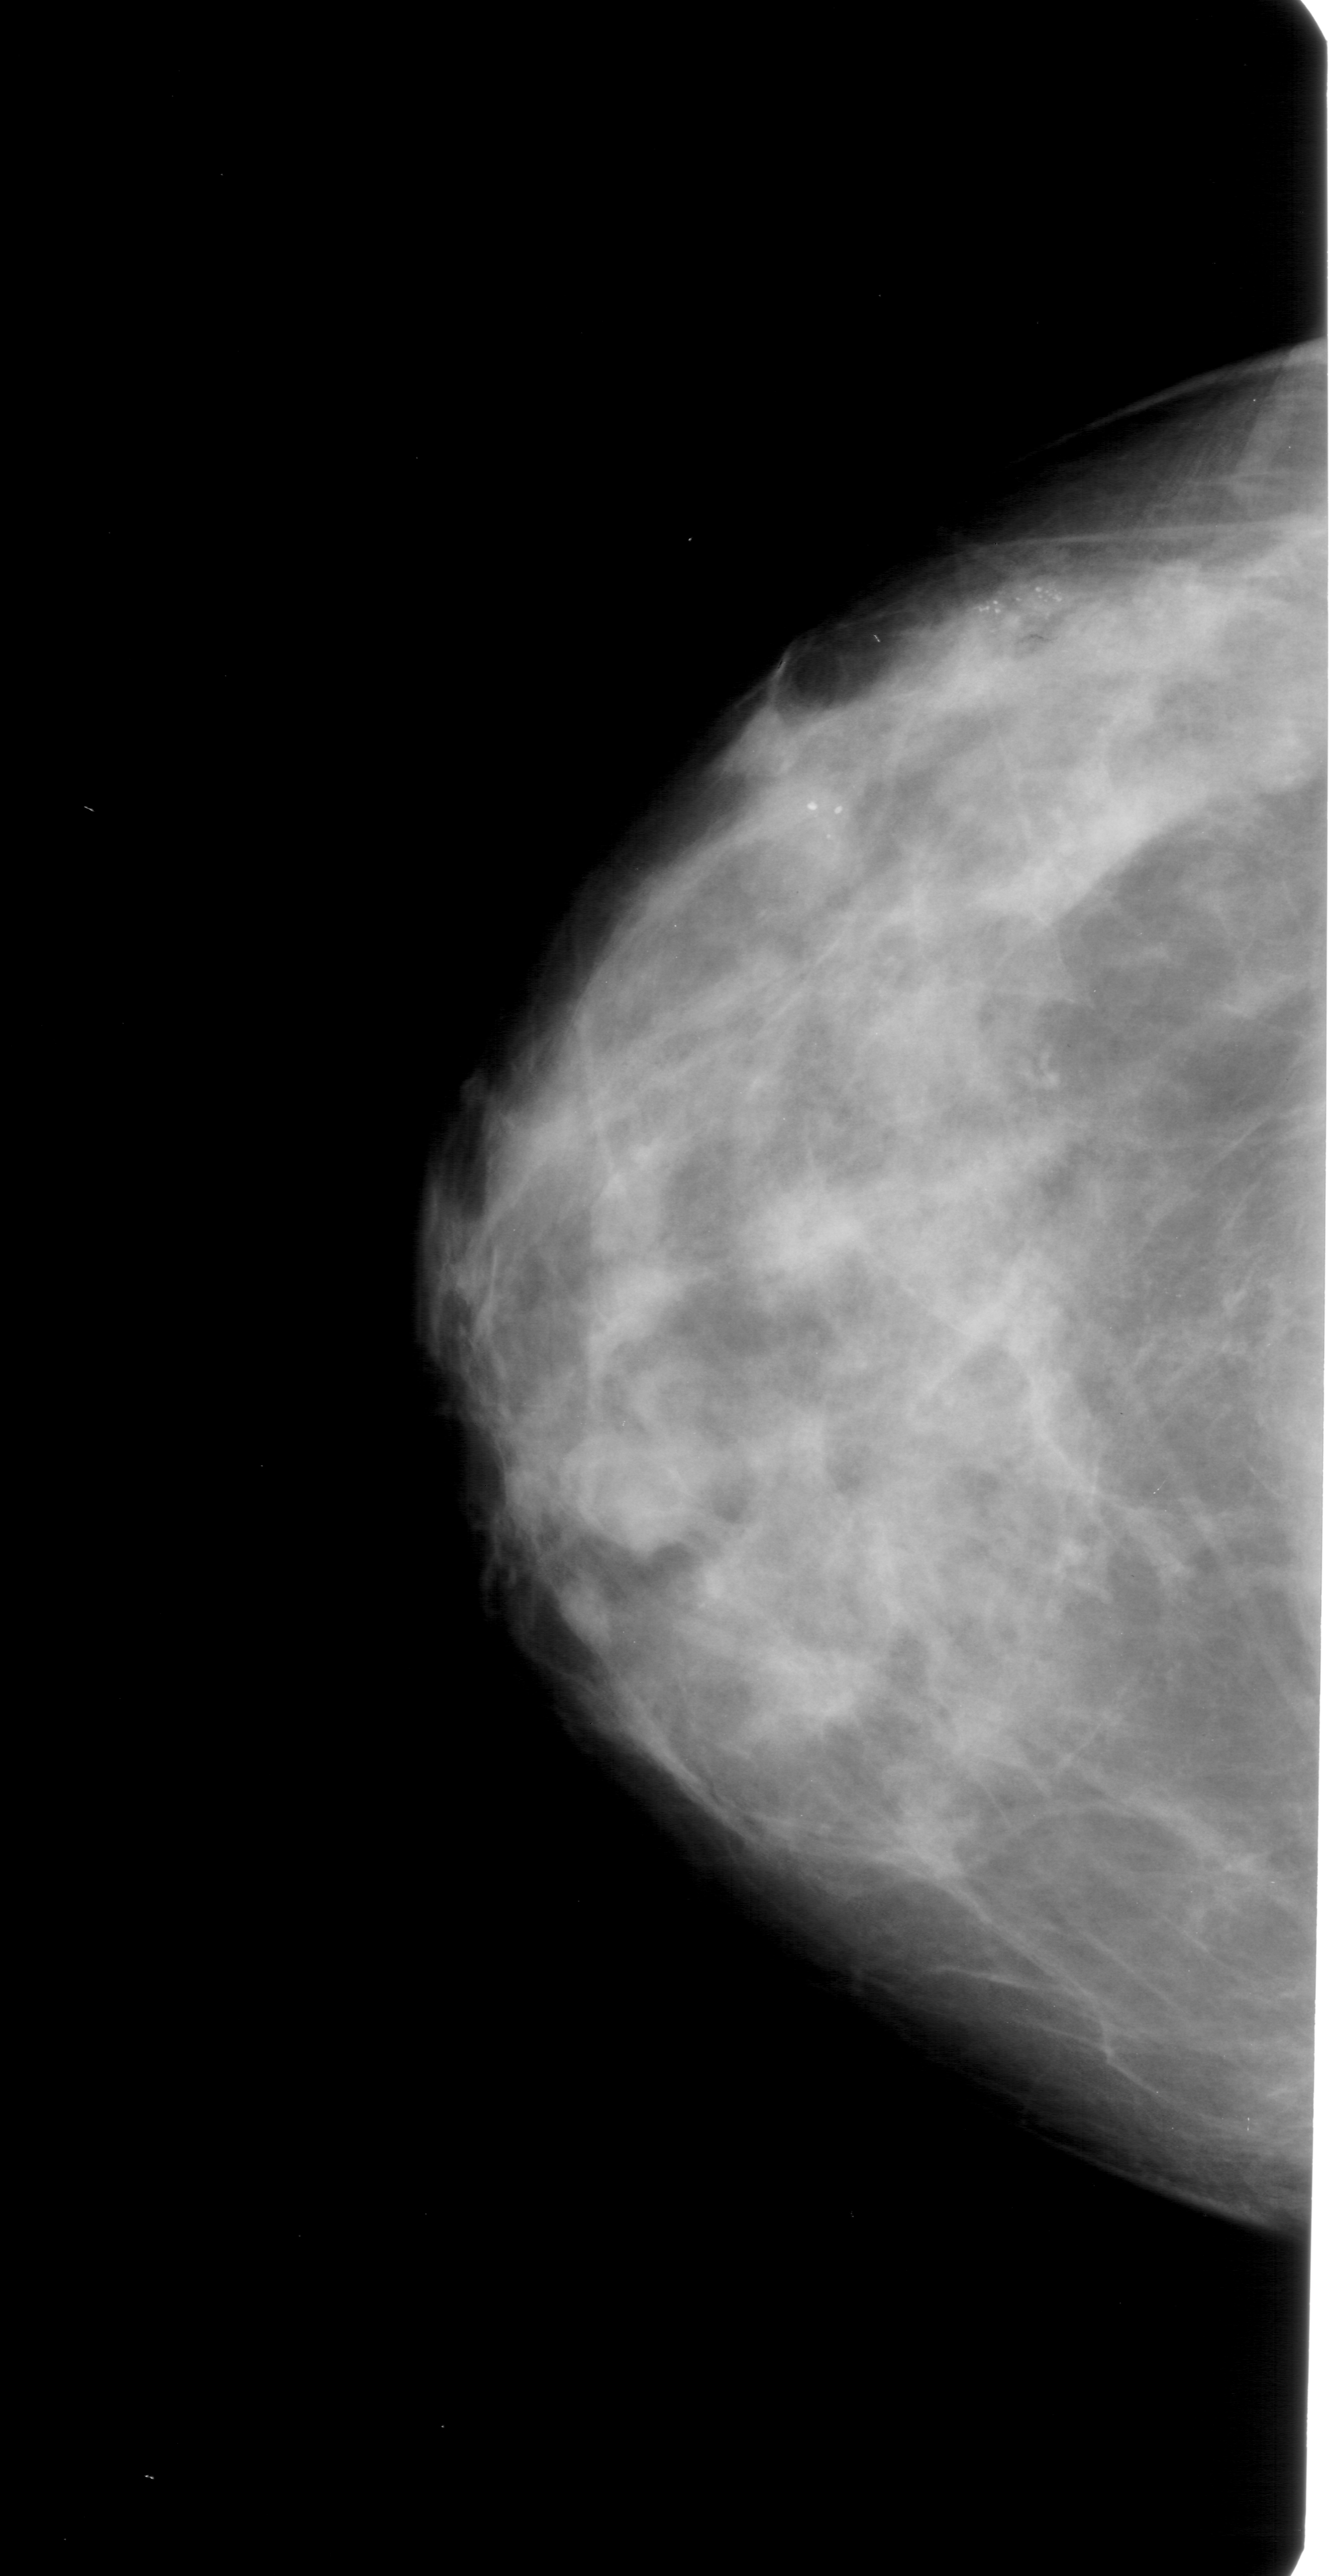
Scanned film-screen mammogram, left breast, craniocaudal (CC) view, breast composition: extremely dense (BI-RADS density category 4 of 4).
- Abnormality record for this image: calcifications, morphology pleomorphic, distribution clustered; BI-RADS assessment category 4; subtlety rating 4 on a 1 (subtle) to 5 (obvious) scale; pathology result (as recorded, not read from the image): malignant.